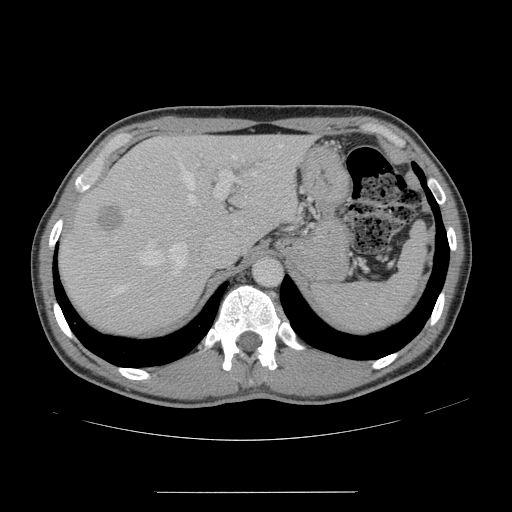
Contrast-enhanced abdominal CT, one axial slice. Position 112 of 178 along the scan axis. 120 kVp. Intravenous contrast given. Soft-tissue window (W 400 / L 40 HU). 512 × 512 image matrix, field of view 401 × 401 mm. Male patient, age 53 years. Case-level facts recorded for this patient, not image findings: diagnosis: colorectal cancer liver metastases, imaged before liver resection; multiple liver metastases: yes; largest metastasis: 2.4 cm; disease in both lobes: no.
Annotated regions visible in this slice (expert manual segmentation):
- hepatic veins: bounding box <114,144,282,294> (left, top, right, bottom; pixels)
- liver: <62,136,308,333>
- planned liver remnant (the part of the liver to remain after resection): <147,136,310,246>
- portal vein (with intrahepatic branches): <129,170,235,213>
- liver metastasis: <98,206,124,232>